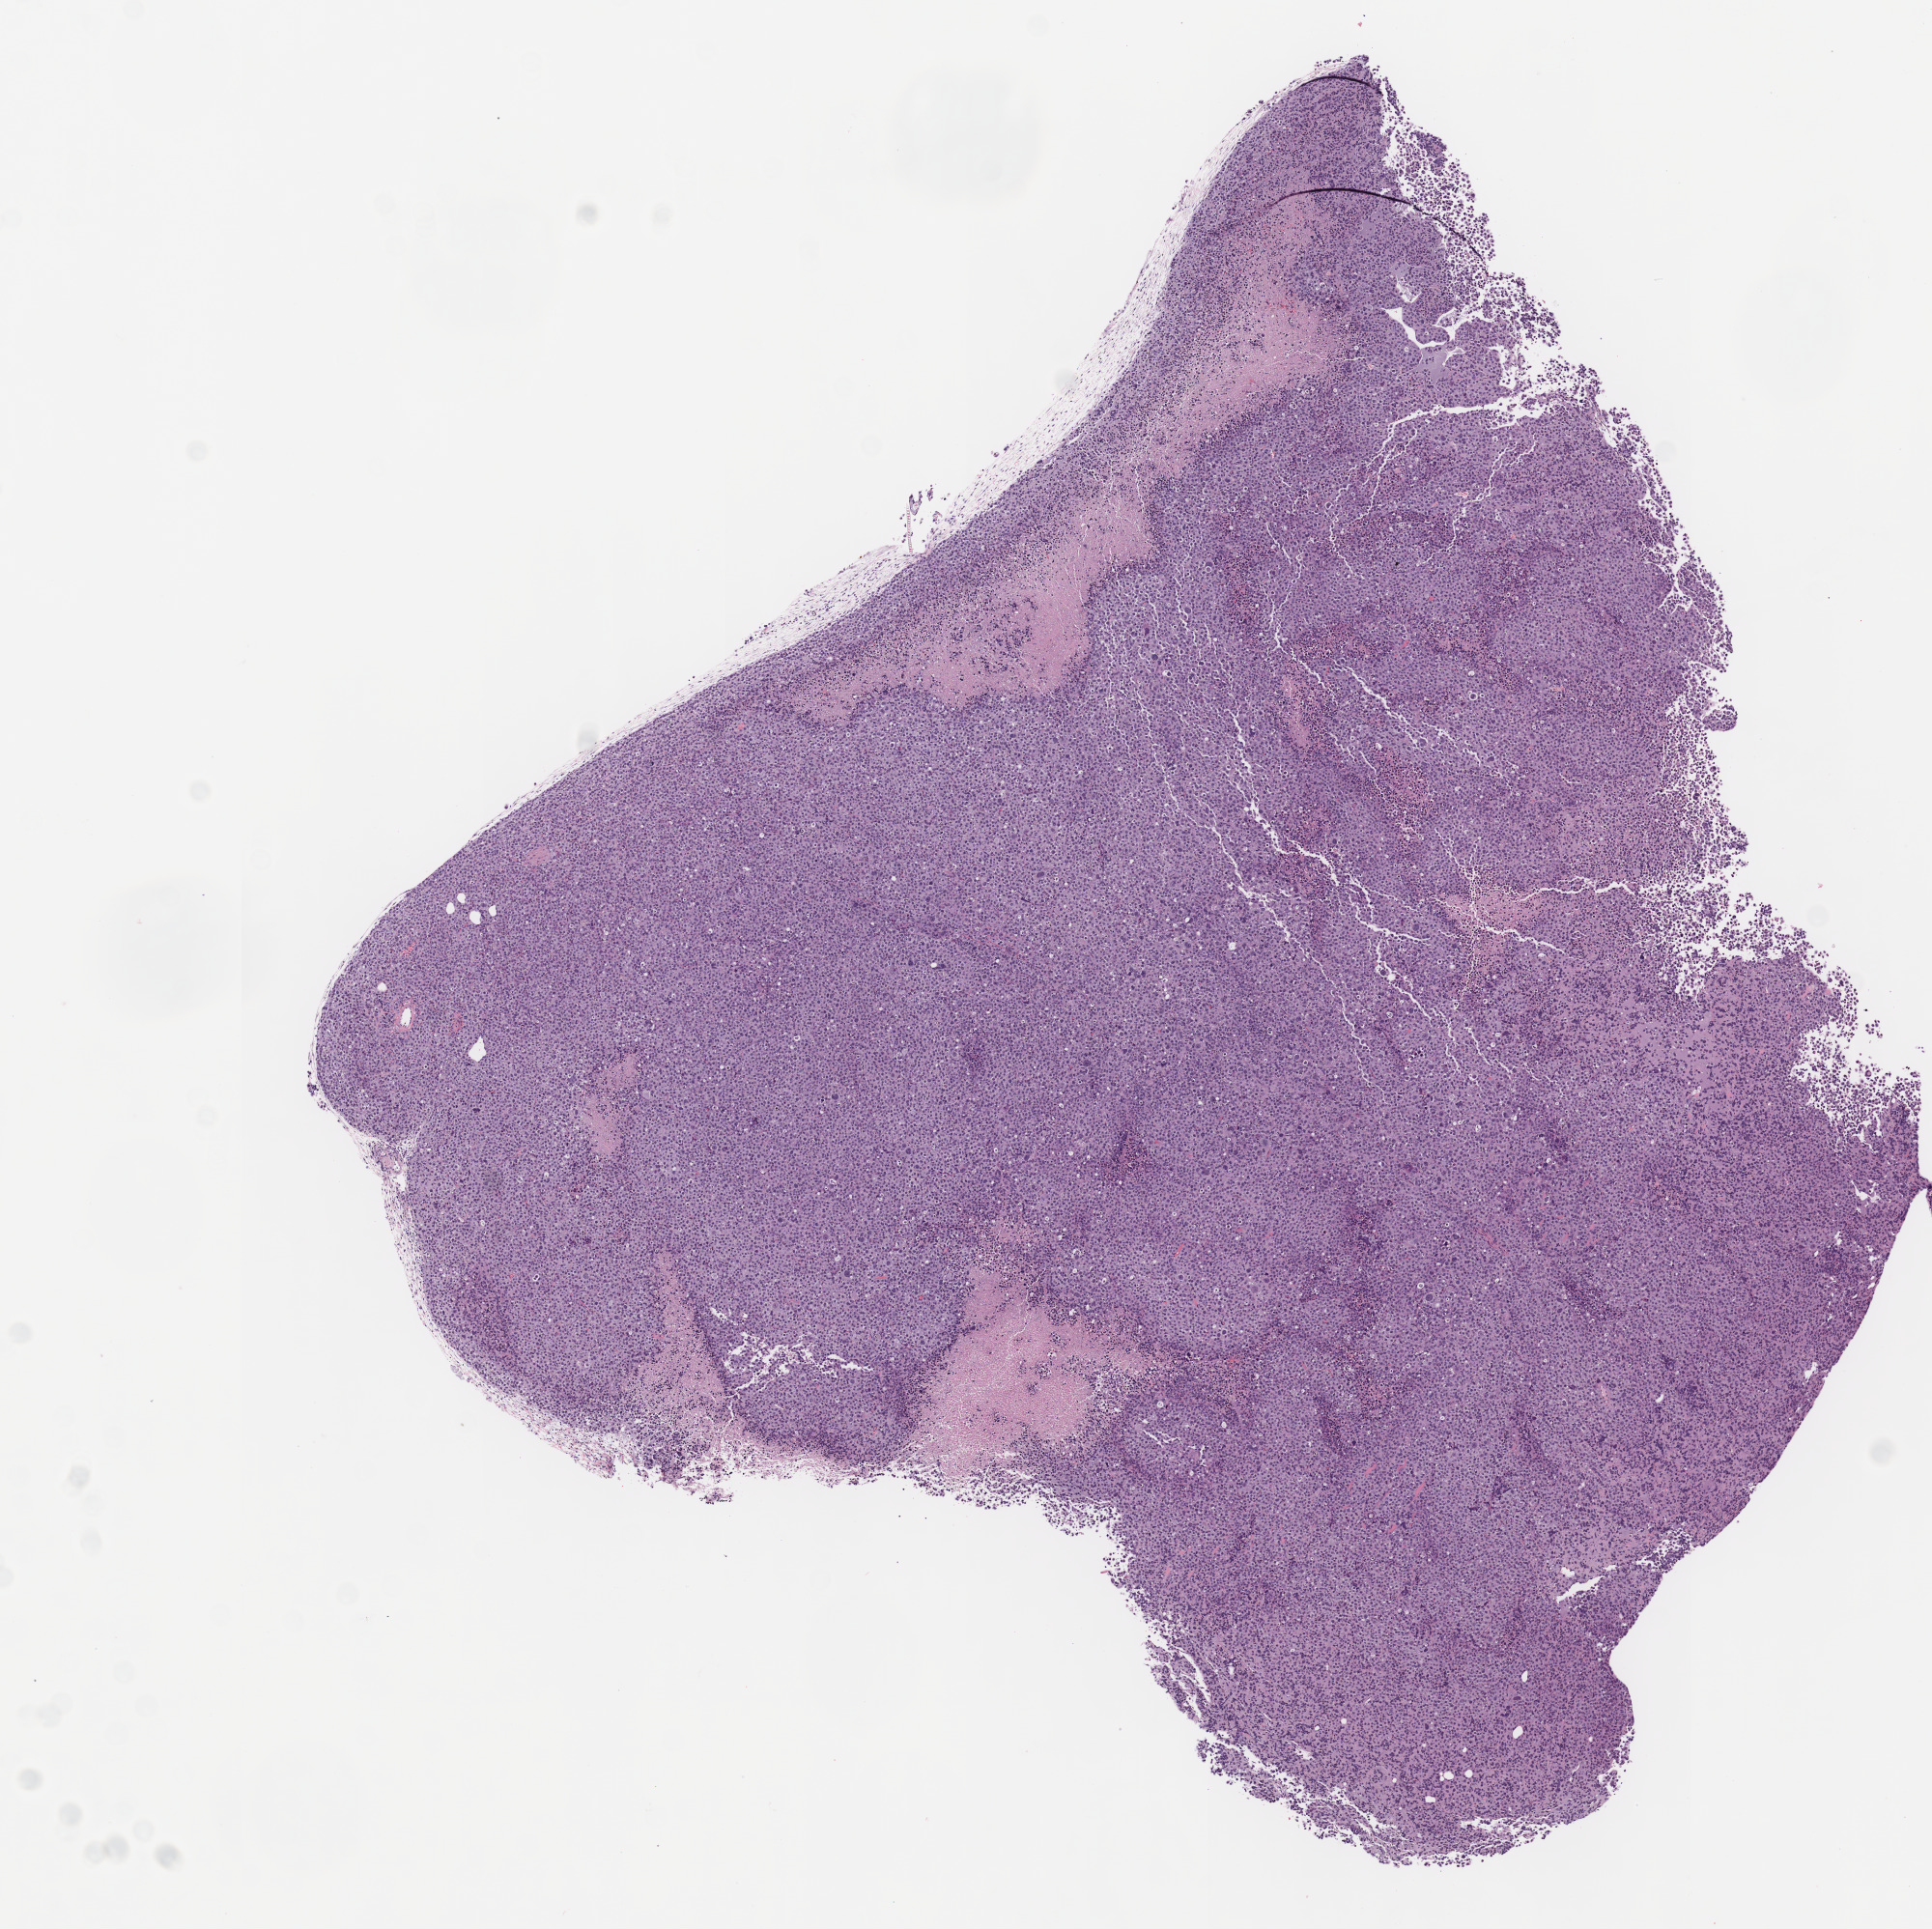
Whole-slide image, haematoxylin and eosin: patient-derived xenograft (human tumor grown in a mouse), passage 4 — a low-resolution overview of the entire scanned area, about 7.9 x 7.9 mm; FFPE section; tumor site category: bladder.
- originating patient diagnosis: Urothelial Carcinoma